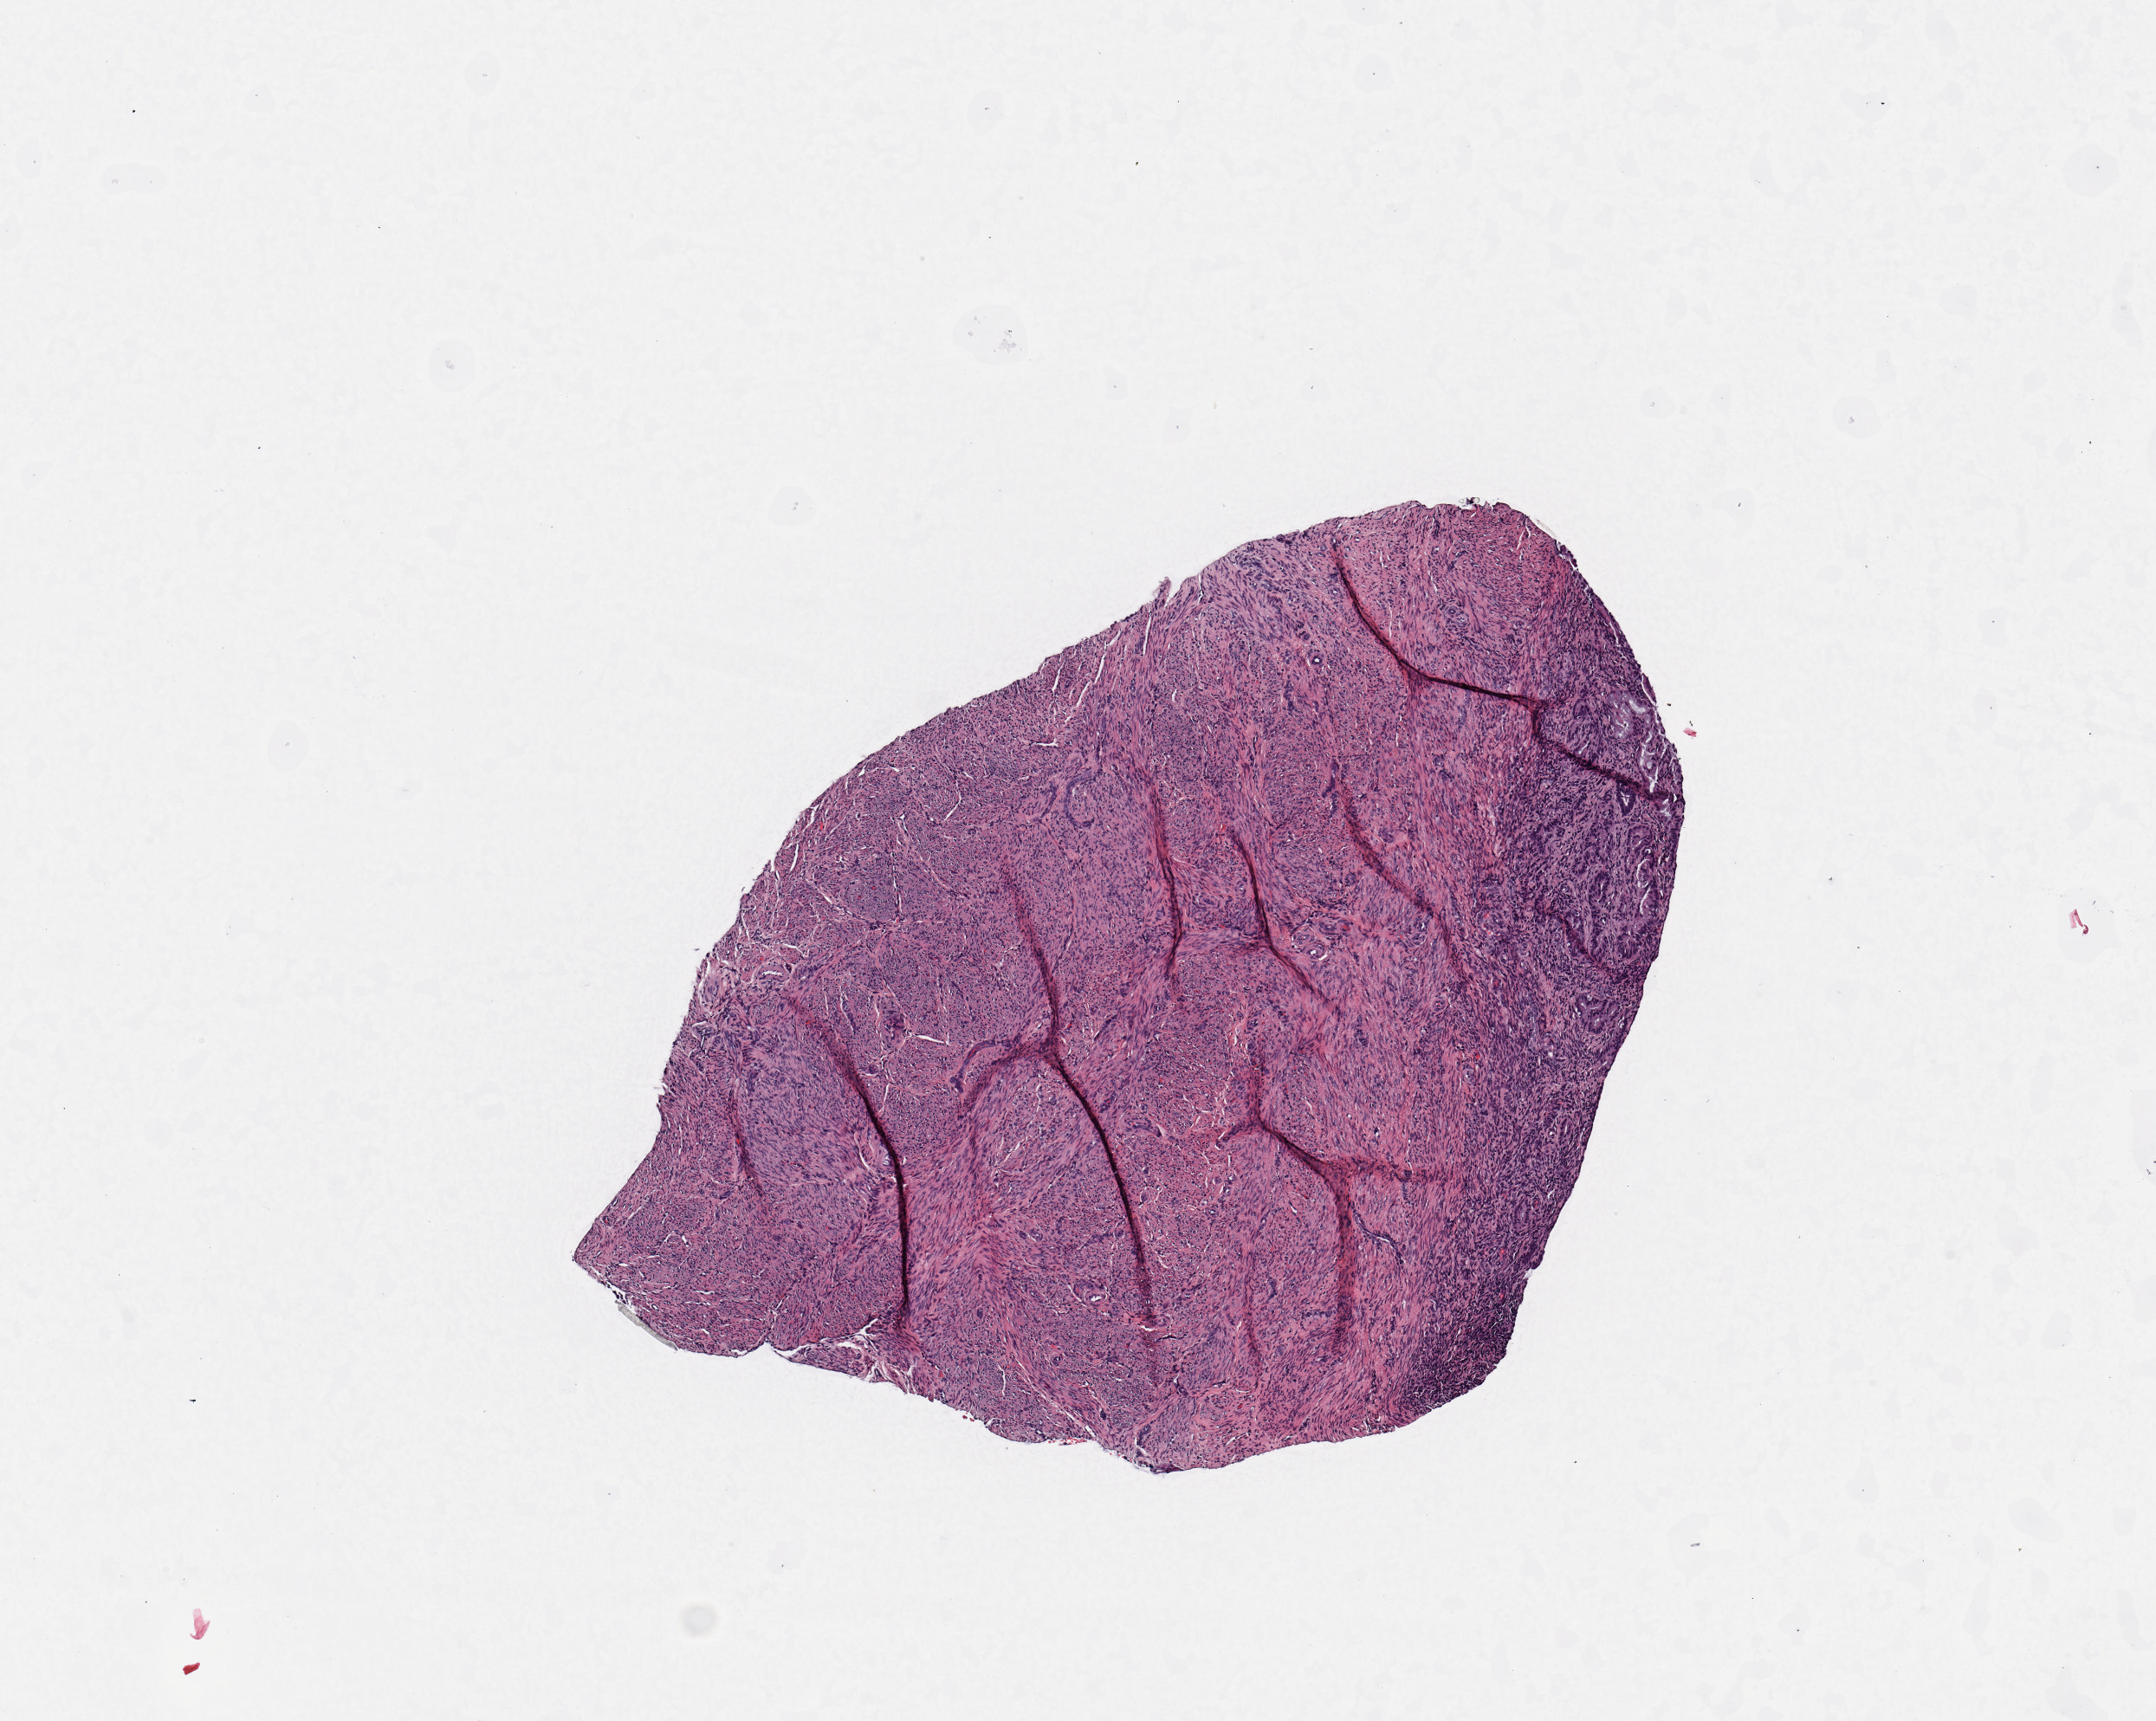
H&E whole-slide image, whole scanned area (about 4.9 x 3.9 mm) shown as a low-resolution overview. Uterus, tumour tissue. Female, 69 y/o. Histologic grade: G2 (moderately differentiated).
- diagnosis: Endometrioid adenocarcinoma, NOS
- AJCC pathologic stage: IA